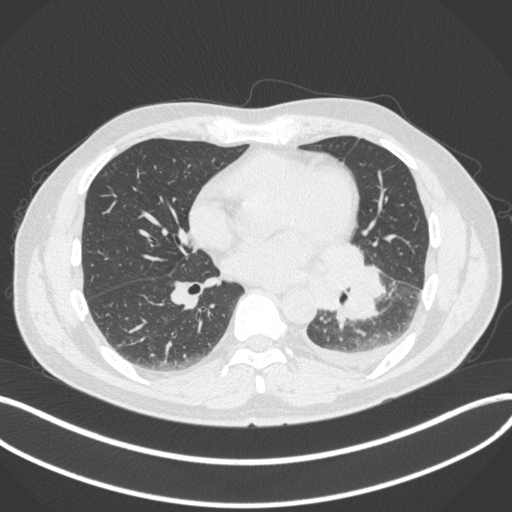
Chest CT, one axial slice. Reconstruction kernel B31f. Lung window (W 1500 / L -600 HU). 512 × 512 image matrix. Male patient, age 58 years. From the clinical record (not read from this slice): clinical TNM (as recorded): T3 N1 M1b.
Outlined on this slice (bounding box drawn by a radiologist):
- lung tumour (recorded histology: small cell carcinoma): bounding box <314,240,390,325> (left, top, right, bottom; pixels)